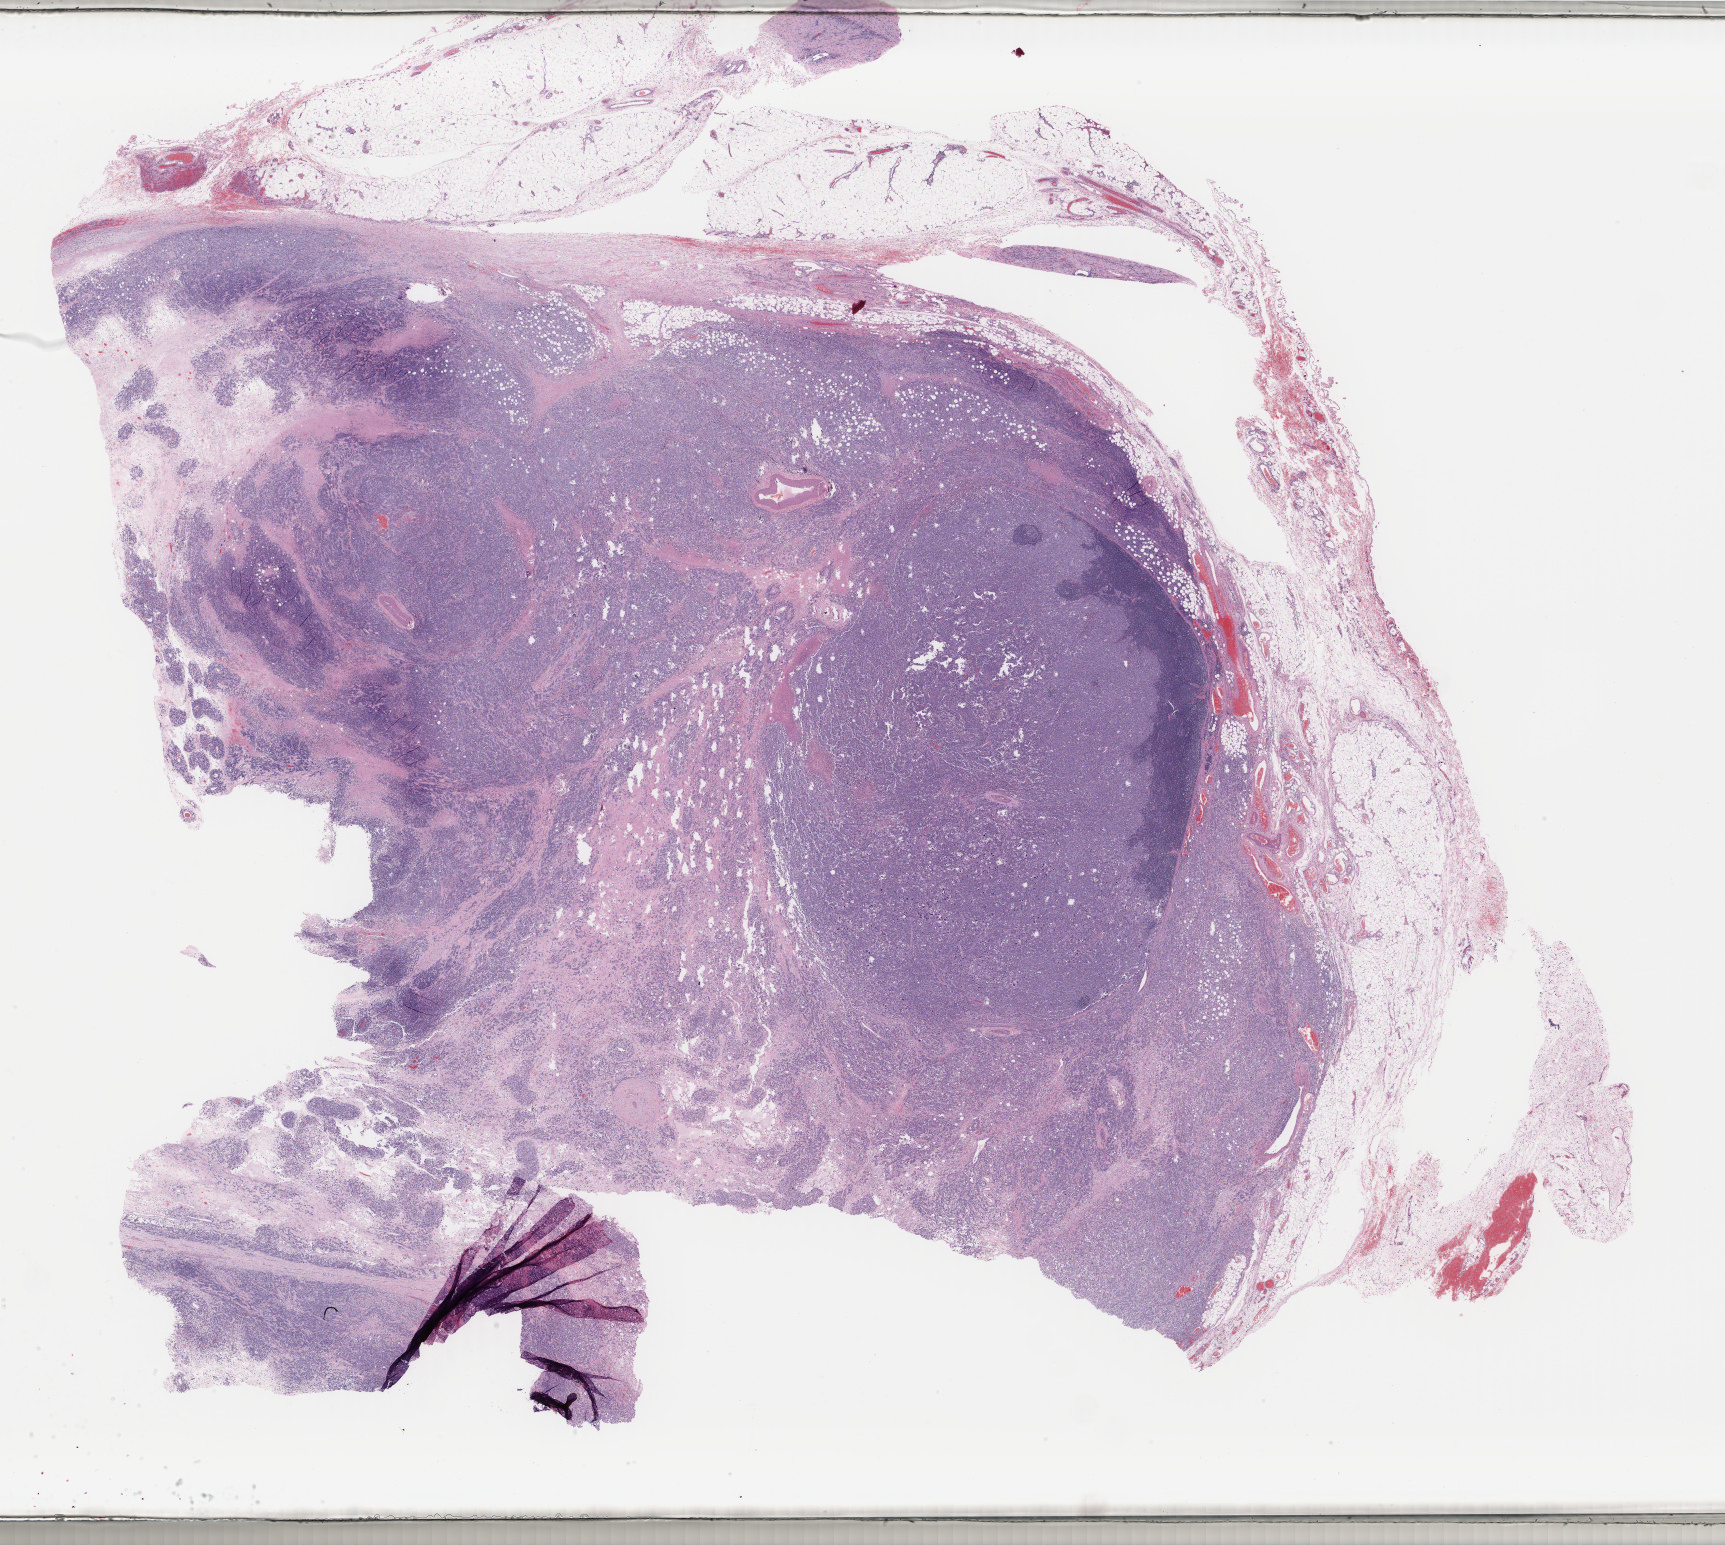
Whole-slide histology image, H&E-stained, low-resolution overview of the scanned area, about 27.4 x 24.5 mm (from a 40x scan); formalin-fixed paraffin-embedded (FFPE) diagnostic section; skin, primary tumour sample. Female, age 36 years at initial diagnosis.
Histologic diagnosis: Malignant melanoma, NOS.